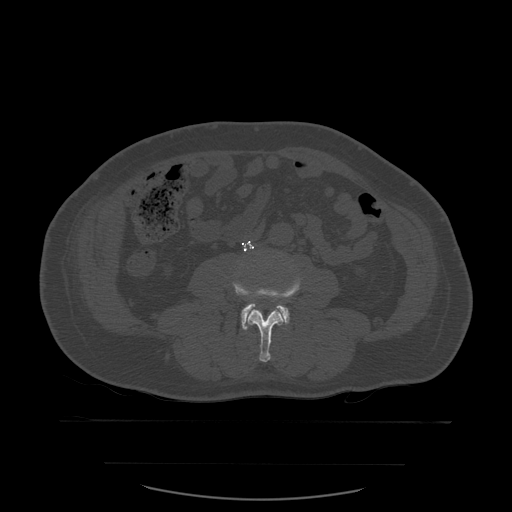
CT including the spine, one axial slice. Position 182 of 590 along the scan axis. Bone window (W 1800 / L 400 HU). 1.25 mm slice thickness. 512 × 512 image matrix, field of view 479 × 479 mm. Patient age 71 years. Case-level facts recorded for this patient, not image findings: primary cancer: lung; vertebrae with lytic lesions (as recorded): T1, T2, L5, S1.
Annotated regions visible in this slice (semi-automatically segmented with operator editing):
- L3 vertebra: bounding box (x1, y1, x2, y2) in pixels: (233, 272, 302, 363)
- L4 vertebra: (241, 303, 290, 330)